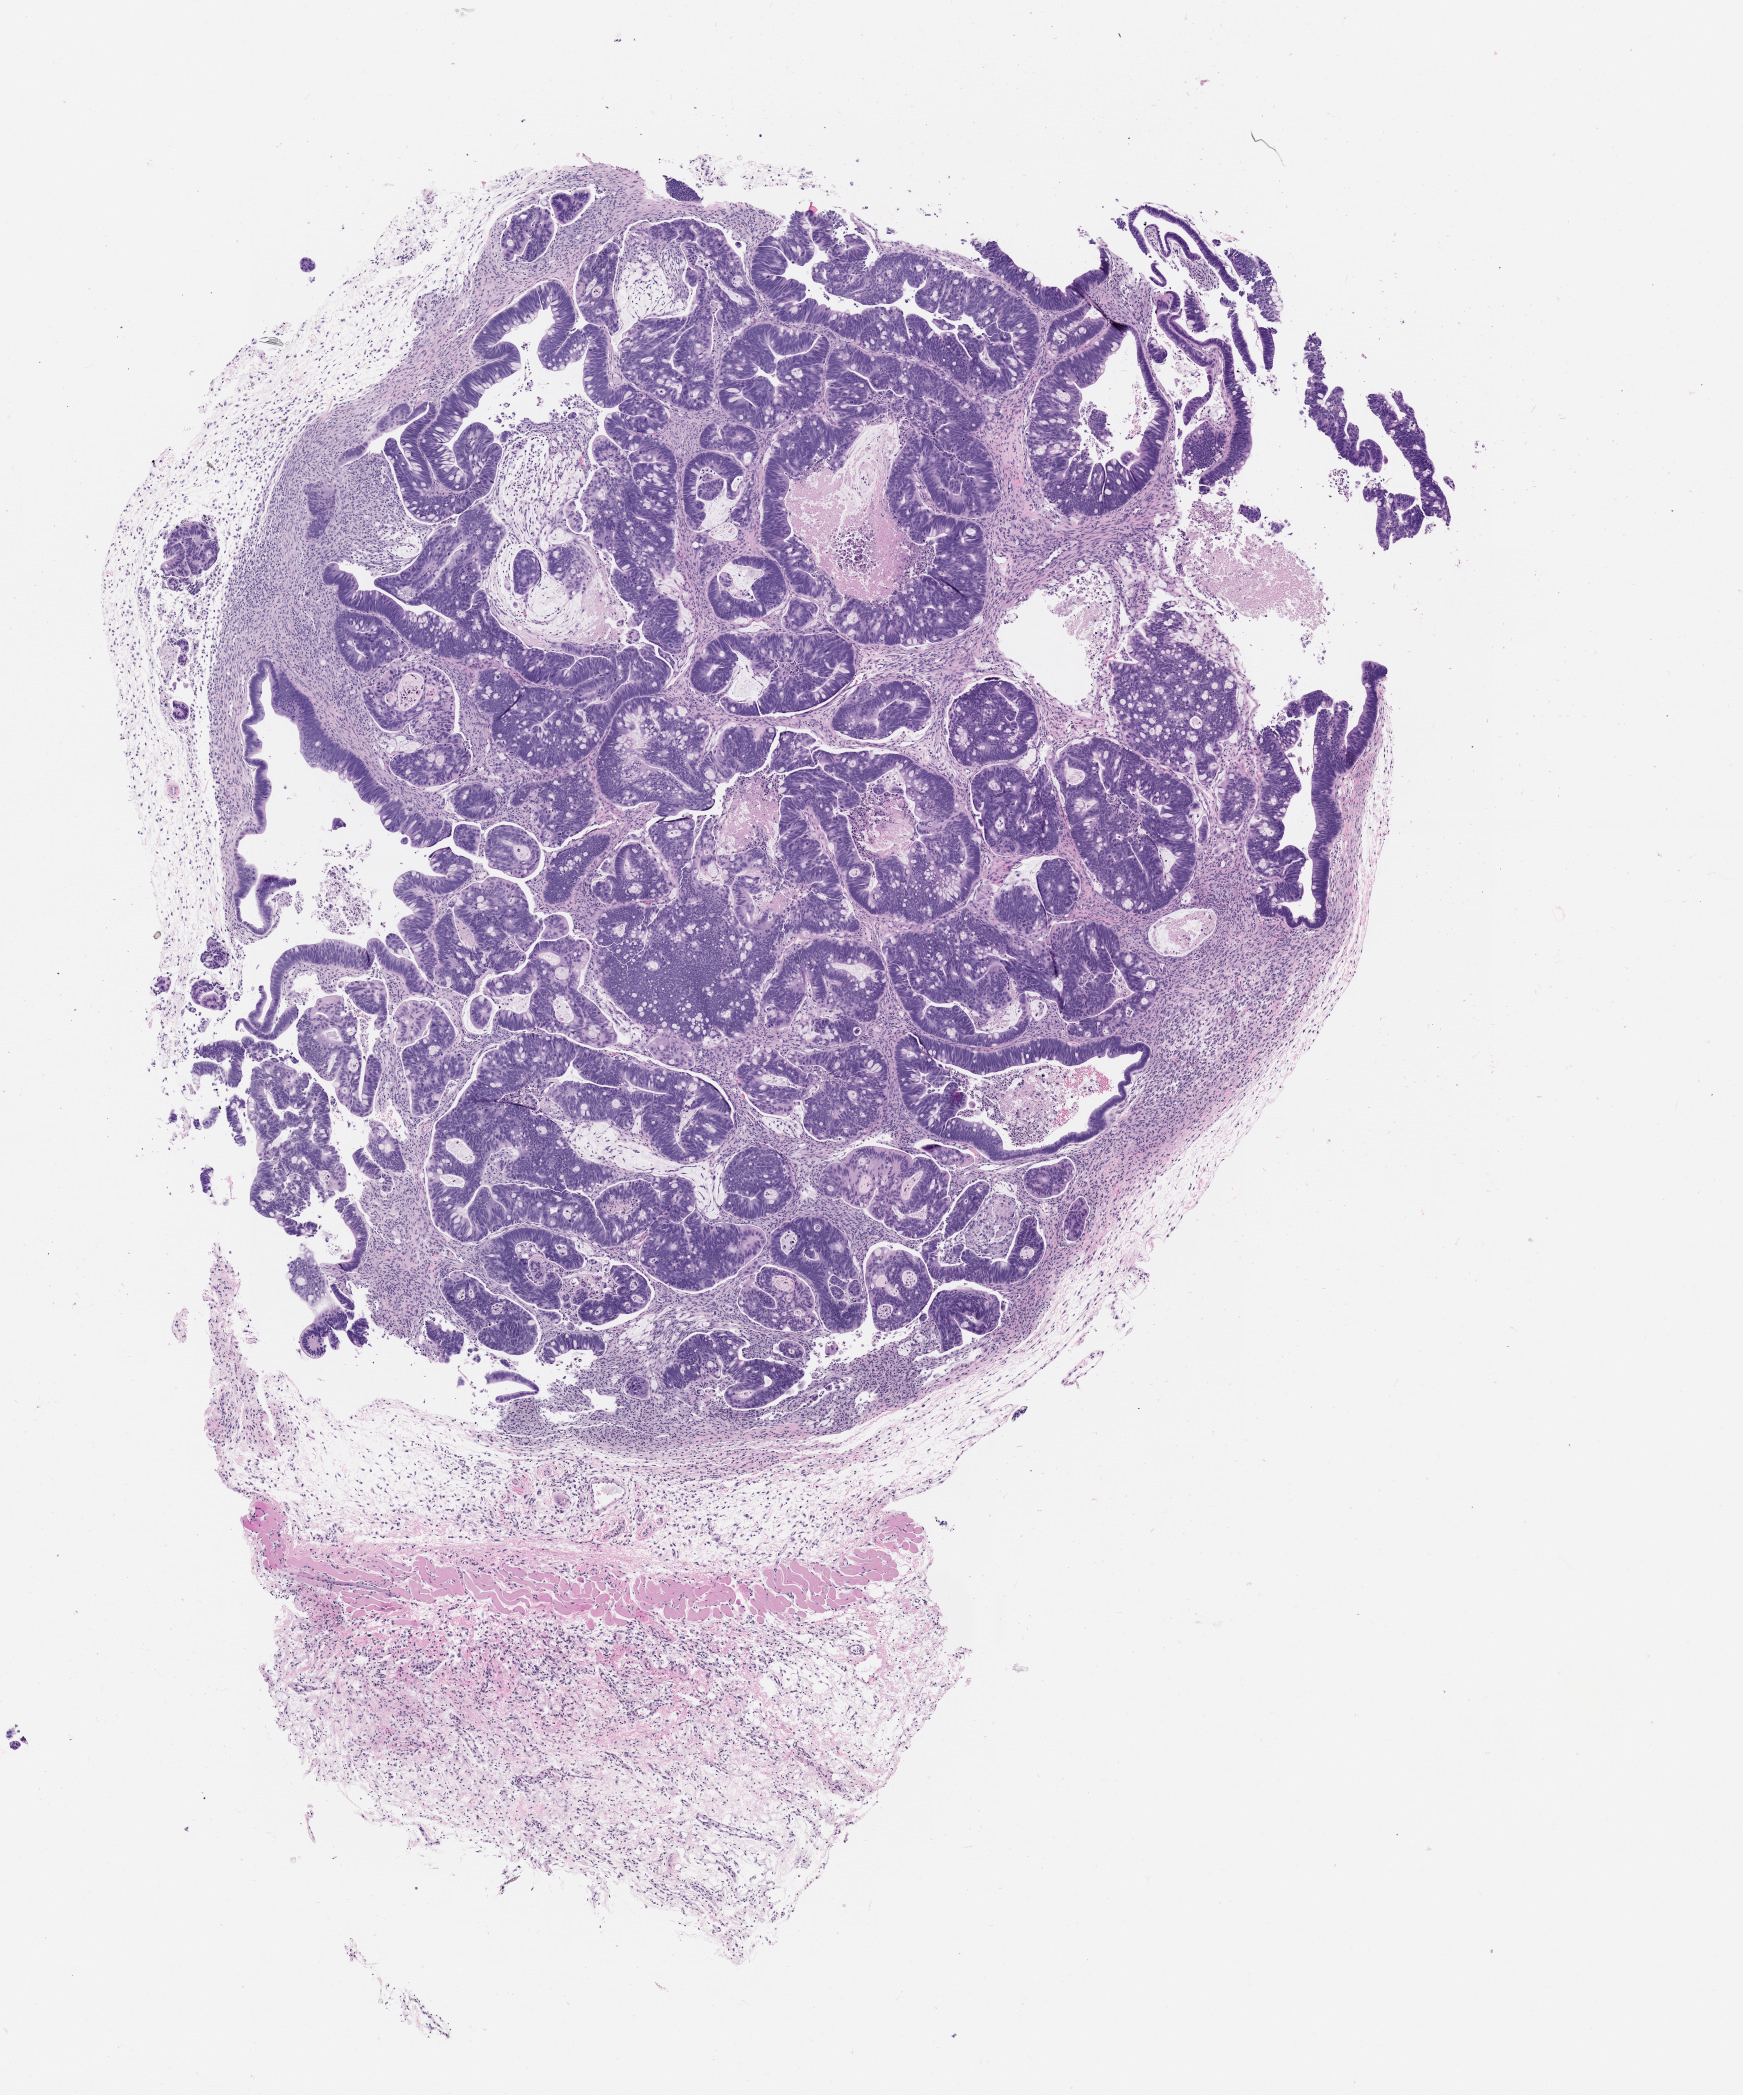
Hematoxylin and eosin (H&E) whole-slide image of a patient-derived xenograft (PDX) tumor grown in a mouse, passage 3 — a low-resolution overview of the entire scanned area, about 7.0 x 8.4 mm. Formalin-fixed paraffin-embedded section. Tumor site category: colon.
- originating patient diagnosis: Colon Adenocarcinoma